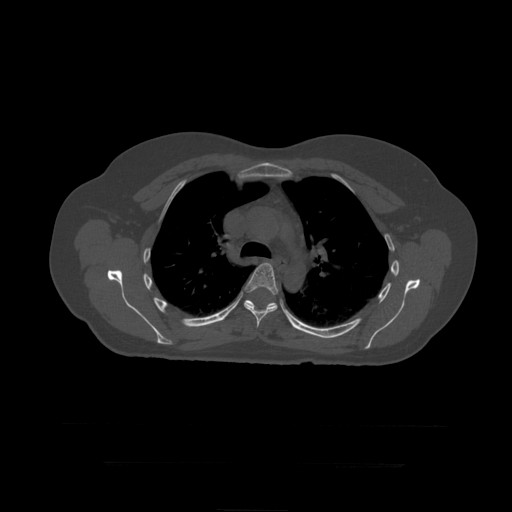
CT including the spine, one axial slice; position 316 of 399 along the scan axis; reconstruction kernel STANDARD; 120 kVp; bone window (W 1800 / L 400 HU); 1.25 mm slice thickness; 512 × 512 image matrix. Patient age 41 years. Case-level facts recorded for this patient, not image findings: primary cancer: breast.
Structures marked on this image (semi-automatic segmentation, software-assisted and operator-edited):
- T6 vertebra: bounding box [x1, y1, x2, y2] px = [244, 263, 279, 328]
- T7 vertebra: [245, 300, 276, 308]